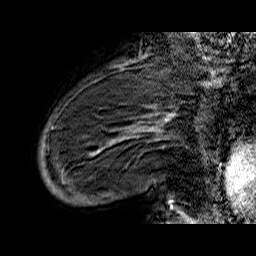
Breast MRI (dynamic contrast-enhanced), one sagittal slice. Slice 10 of 60 in the series (ordered by position). Dynamic contrast-enhanced series, time point 2 of 6 at this slice position (early post-contrast). 1.5 T. TE 6.5 ms, TR 32.9 ms. 4 mm slice thickness. 256 × 256 image matrix. Female patient. From the clinical record (not read from this slice): setting: breast cancer imaged before/during neoadjuvant chemotherapy; receptor status: HR-positive, HER2-negative.
Annotated regions visible in this slice (semi-automatically segmented with operator editing):
- analysis volume of interest (the breast-tissue region the enhancement analysis was run in; not a lesion): bounding box [x1, y1, x2, y2] px = [39, 74, 176, 210]
- tumour enhancement mask (voxels above the 100 % enhancement threshold inside the analysis volume of interest): [94, 115, 173, 209]